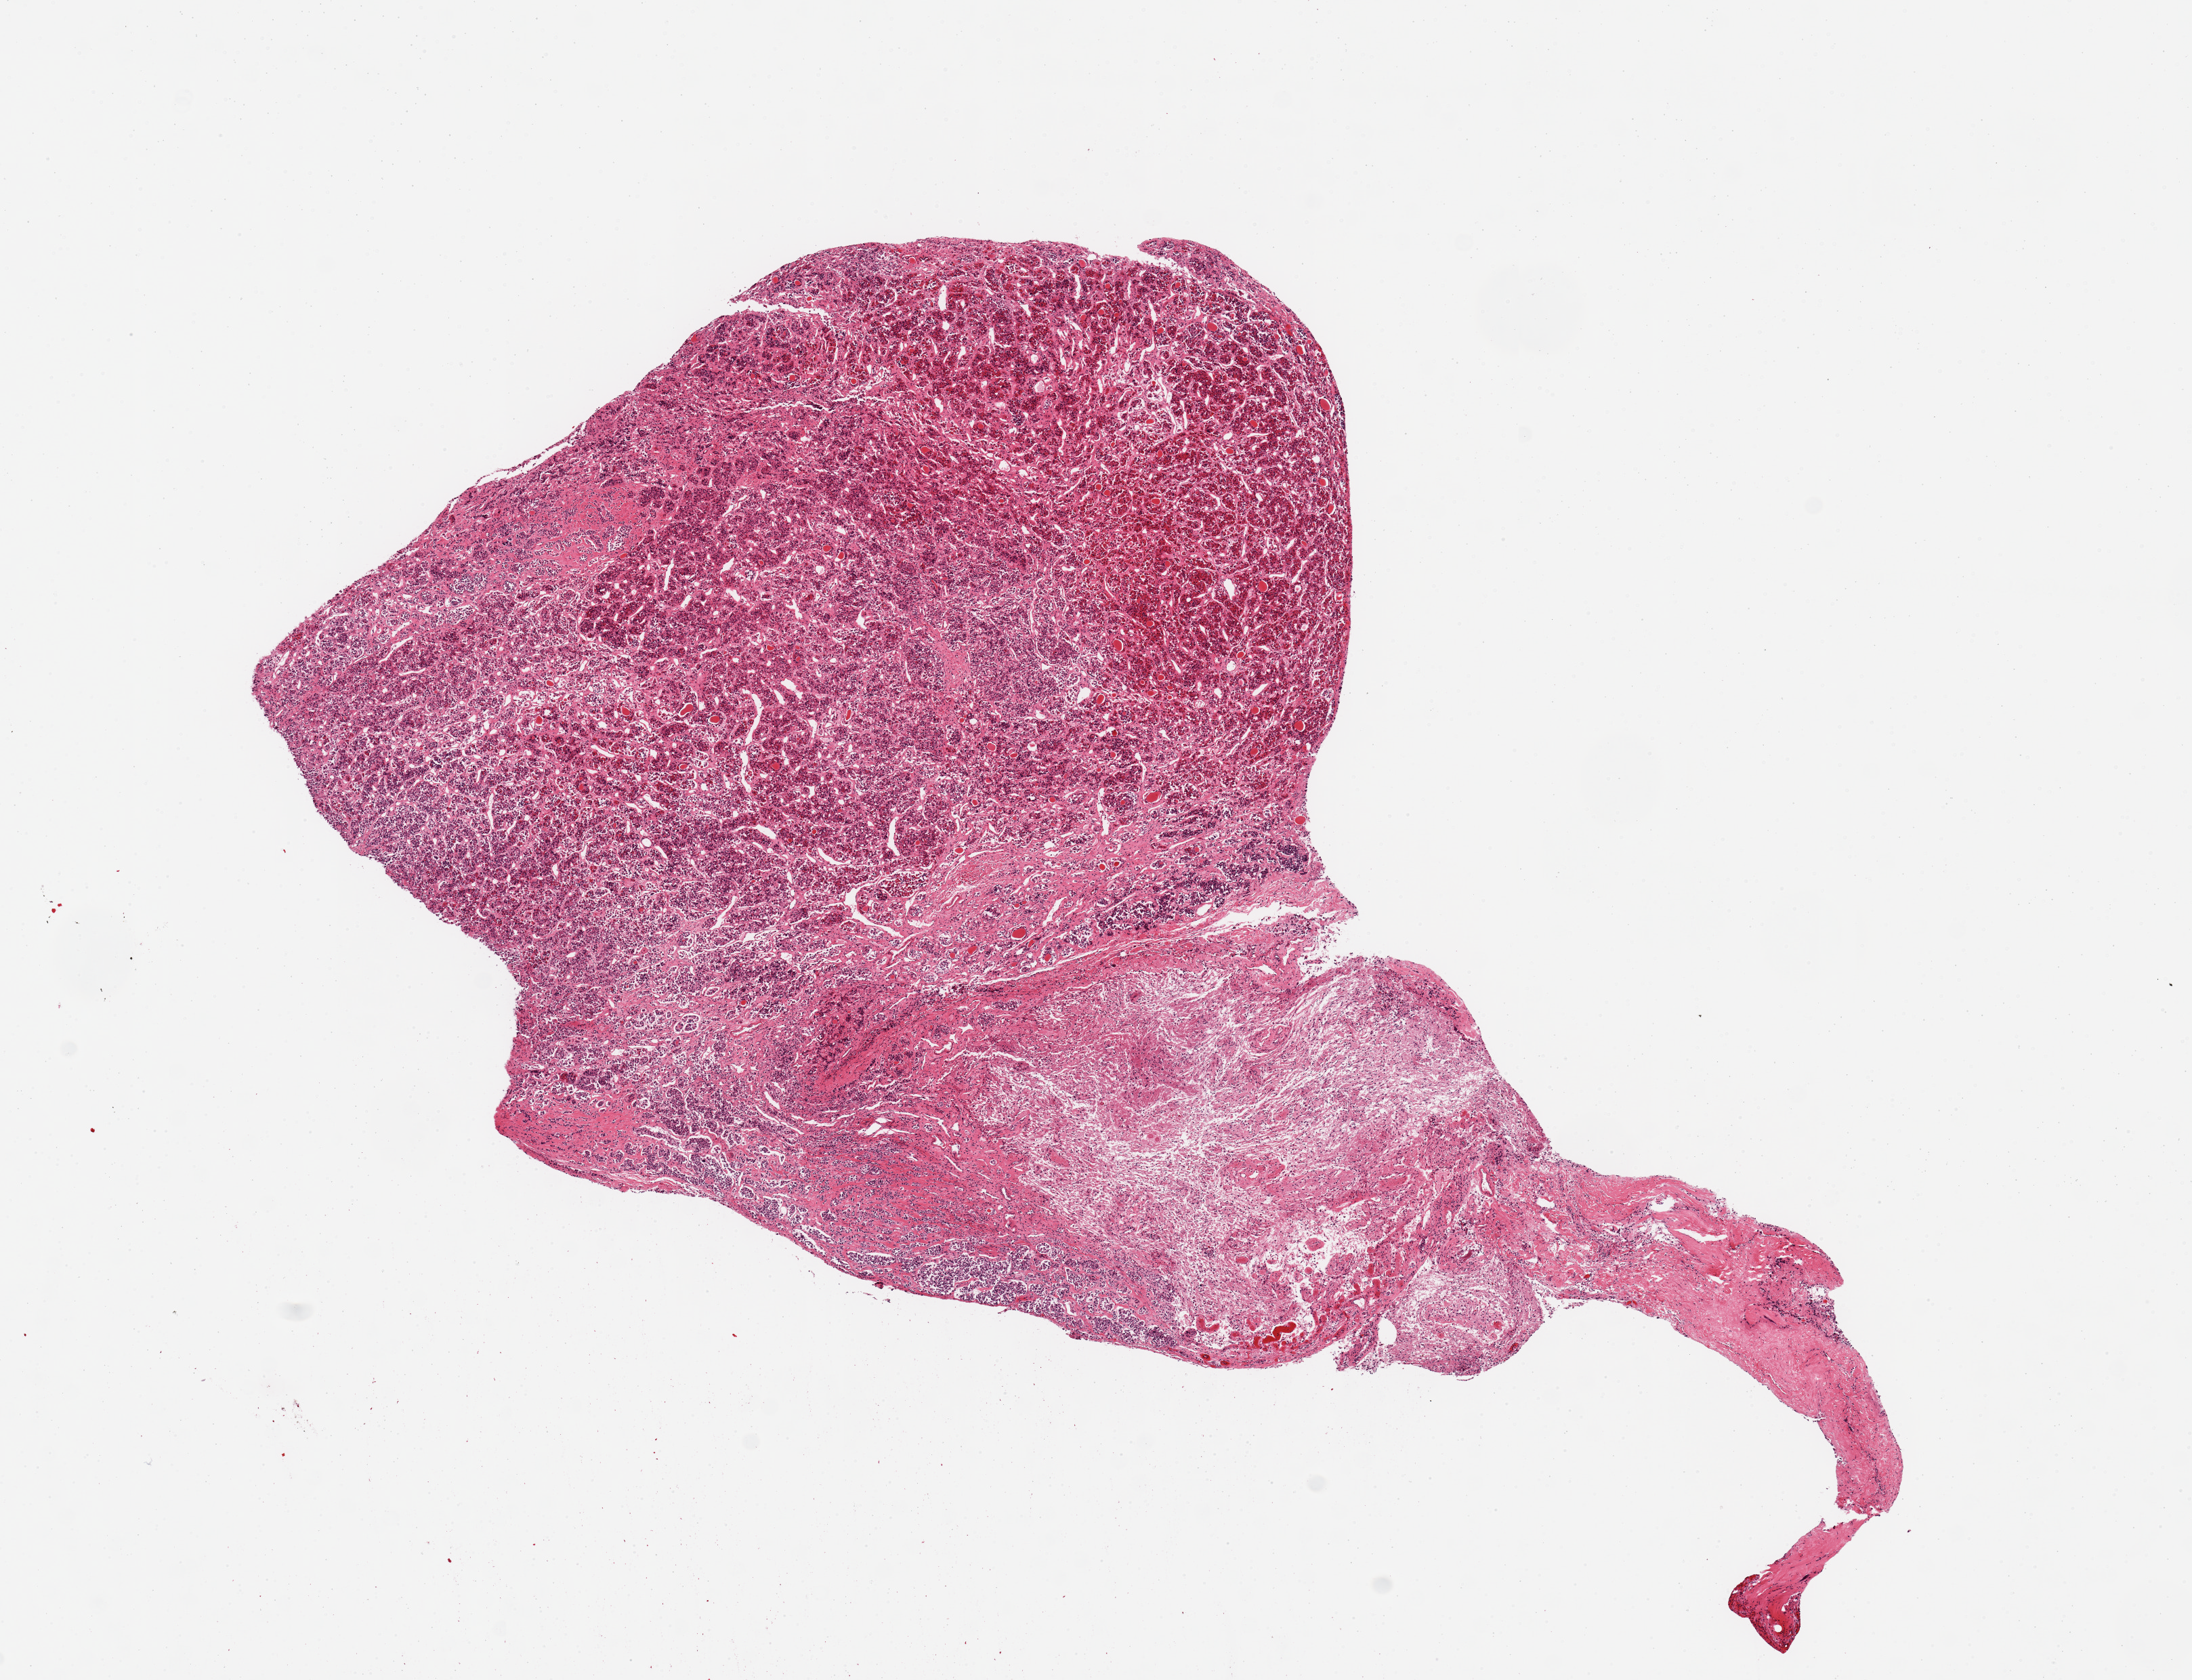
Whole-slide image, H&E stain, whole scanned area (about 12.8 x 9.8 mm, slide scanned at 20x) shown as a low-resolution overview, PAXgene-fixed, paraffin-embedded tissue, sampled site (target tissue): pituitary, tissue donor sample. Donor sex: female.
Review note (as recorded): 1 piece, adenohypophysis and neurohypophysis.